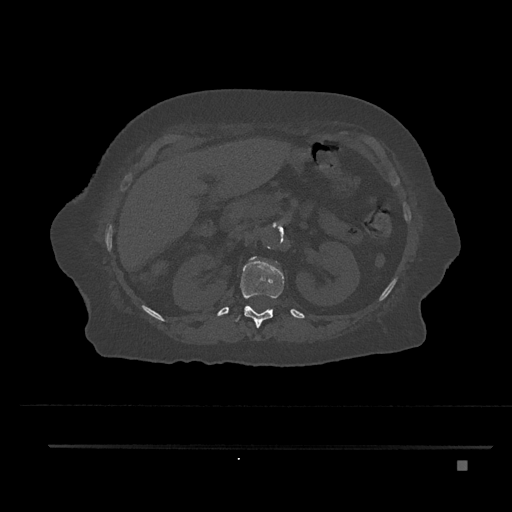
CT including the spine, one axial slice; slice 256 of 797 in the series (ordered by position); reconstruction kernel Br40s/3; bone window (W 1800 / L 400 HU); 0.5 mm slice thickness; 512 × 512 image matrix, field of view 437 × 437 mm. Patient: female, 76 years. From the clinical record (not read from this slice): primary cancer: lung.
Outlined on this slice (semi-automatically segmented with operator editing):
- L1 vertebra: box from (x=249, y=257) to (x=259, y=263) px
- T12 vertebra: (x=235, y=260)–(x=284, y=328)